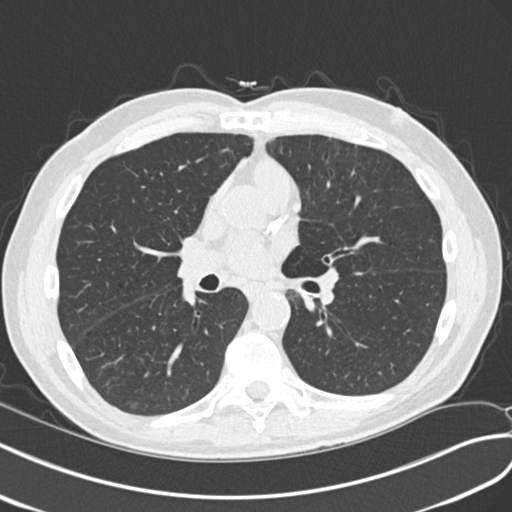
Axial slice from a low-dose chest CT screening exam, second screening round (one year after baseline), lung window (W 1500 / L -600 HU), 2 mm slice thickness, standard (soft-tissue) reconstruction kernel (B30f), slice 110 of 240 in the series. Male, age 68 years at enrolment. Current smoker at enrolment.
Expert reader's lesion annotation, box from (x=105, y=381) to (x=156, y=420) px. The screening reader recorded 4 non-calcified nodules or masses ≥4 mm on this exam (right upper lobe, left upper lobe, right upper lobe, right lower lobe); which of them this box marks is not recorded. Official screen result: positive, other. Lung cancer was diagnosed 653 days after this screen: non-small cell carcinoma, right lower lobe, poorly differentiated (G3), stage IA (AJCC 6th edition), 23 mm at pathology.